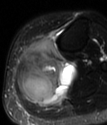
MRI of an extremity soft-tissue mass, one axial slice; position 34 of 78 along the scan axis; T2-weighted fat-saturated; MR volume resampled by the dataset authors to the PET/CT grid (not the native acquisition matrix); 3.27 mm slice thickness; 107 × 125 image matrix, field of view 104 × 122 mm. Female patient. From the clinical record (not read from this slice): histological type: extraskeletal high grade osteogenic sarcoma; grade: high; site of the primary tumour: left calf.
Outlined on this slice (expert contour drawn on MRI and transferred to this co-registered scan by the dataset authors):
- gross tumour volume (mass): box from (x=17, y=40) to (x=75, y=105) px